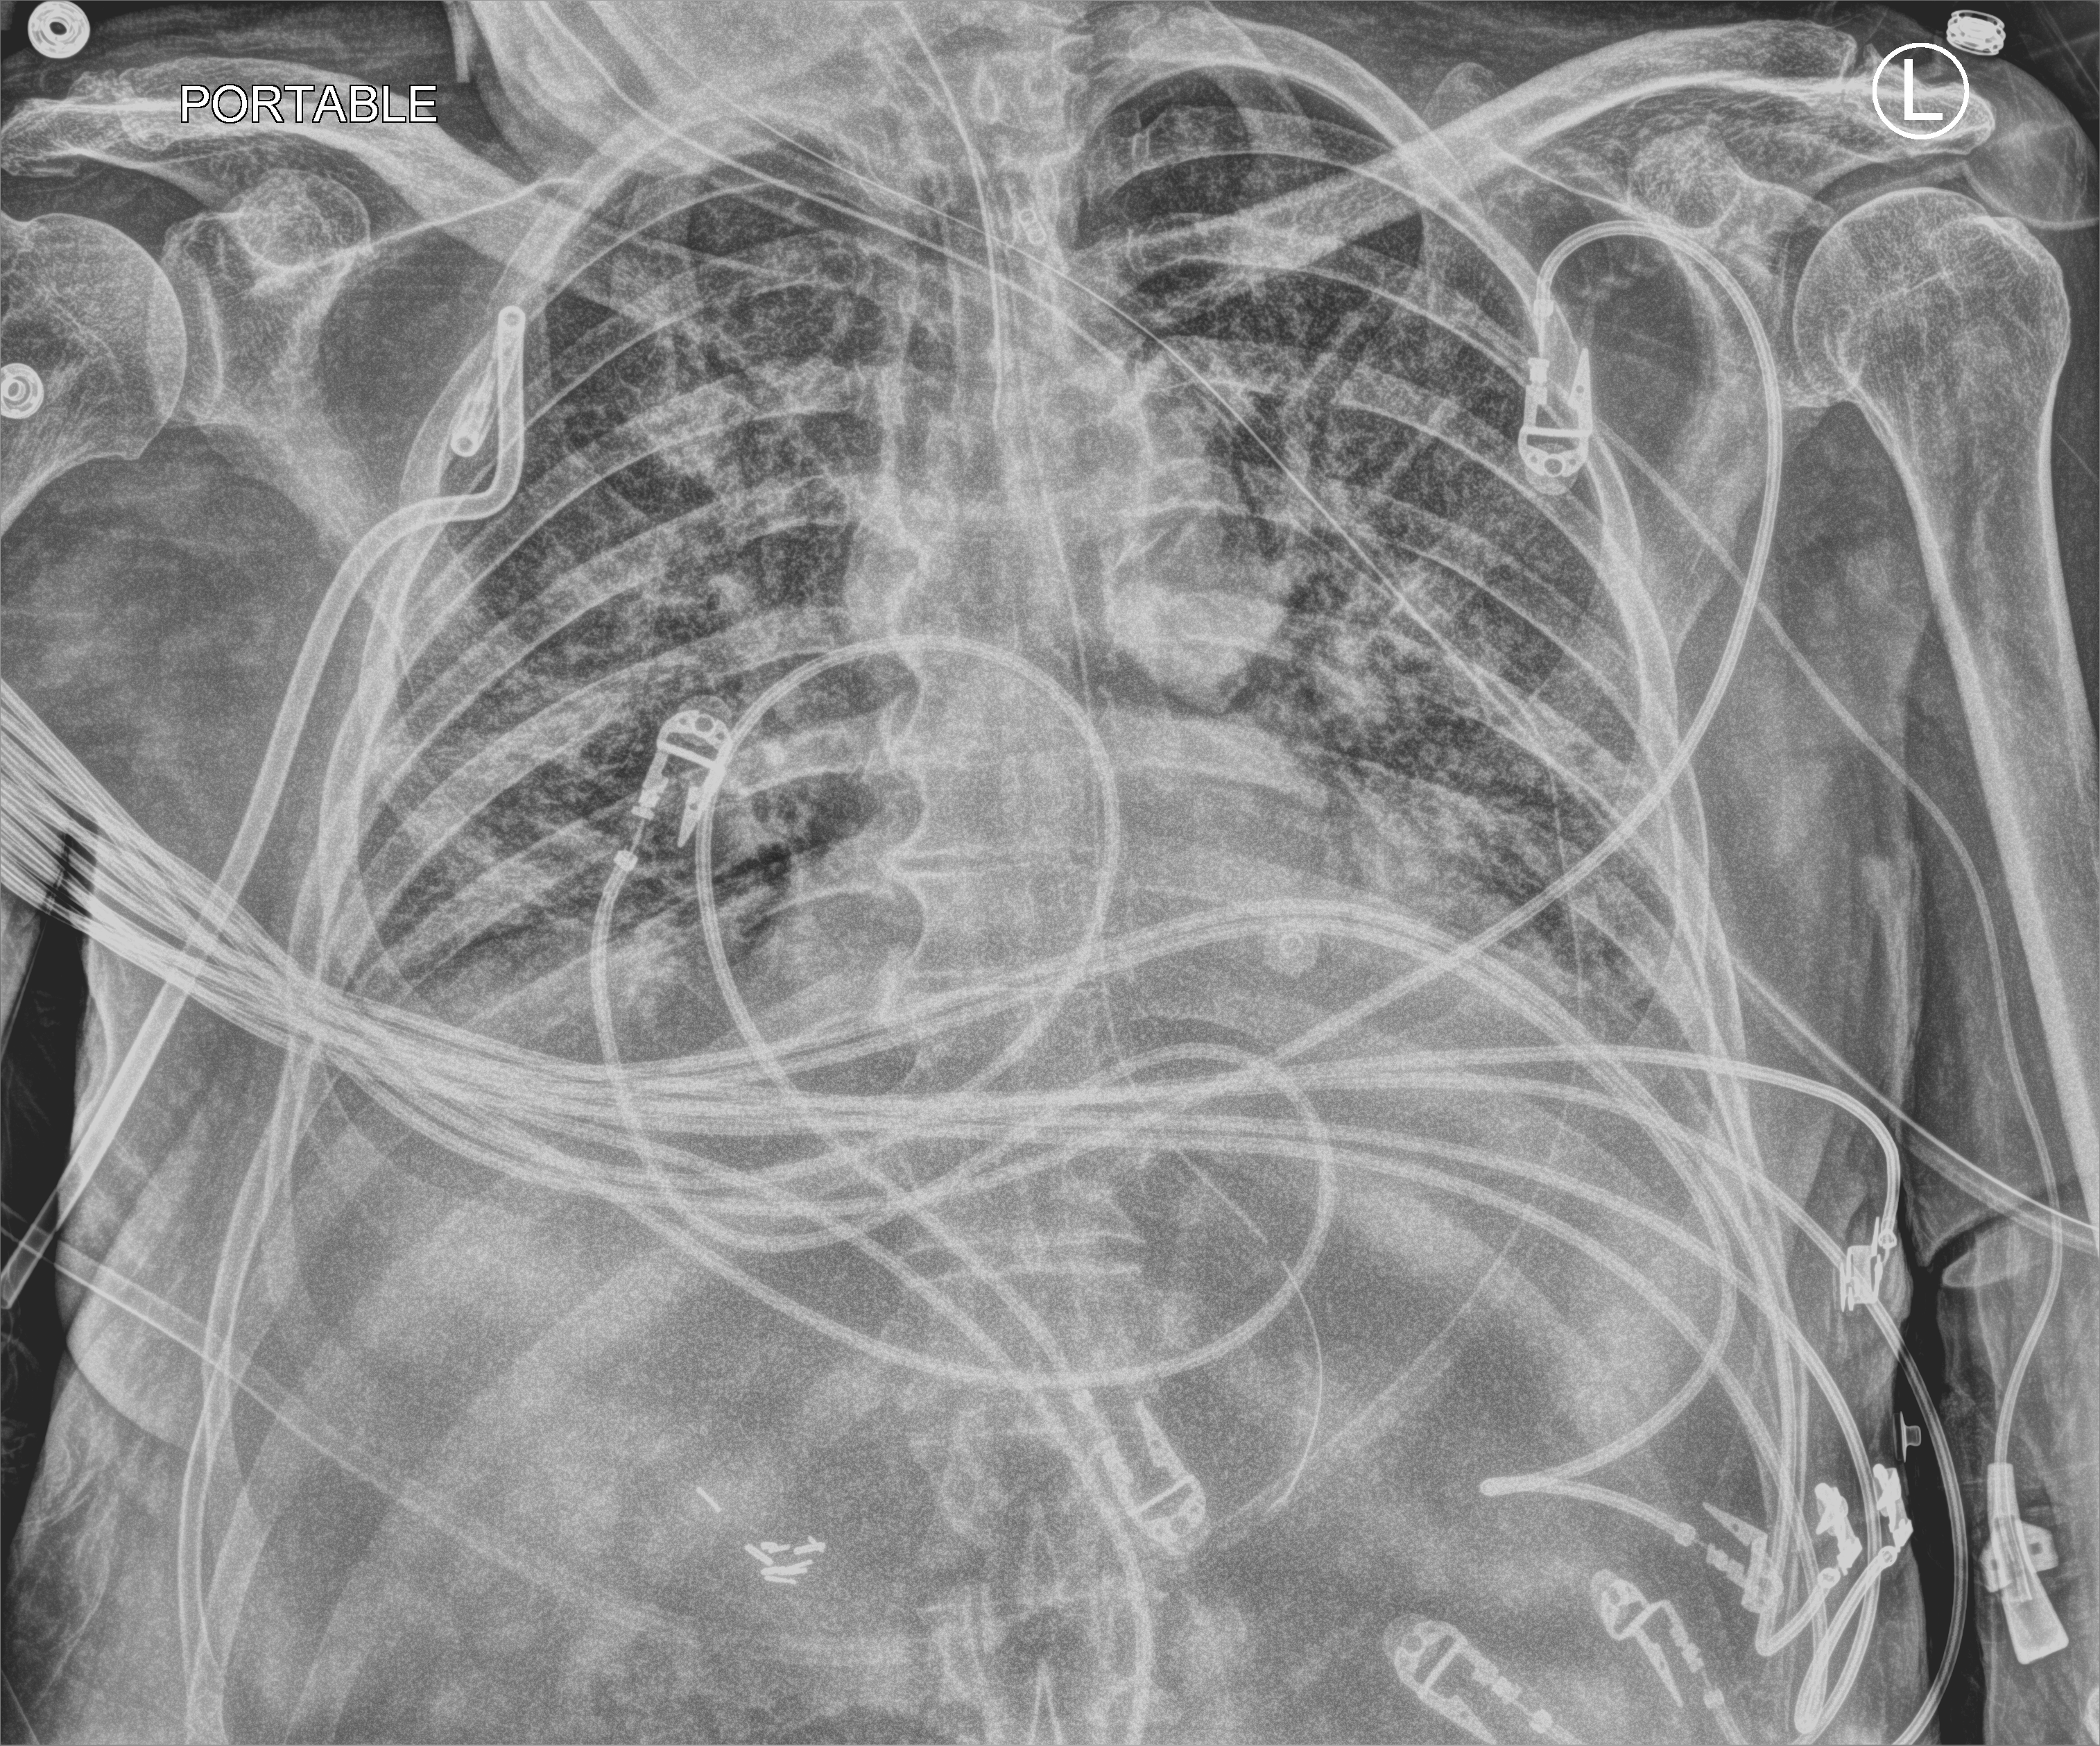
Bedside chest radiograph (computed radiography); anteroposterior (AP) projection. Male patient hospitalised with COVID-19, age 75–90 years.
Admission-level facts for this patient (not findings on this image; timing relative to this image not recorded):
- admitted to intensive care during this hospital stay: yes